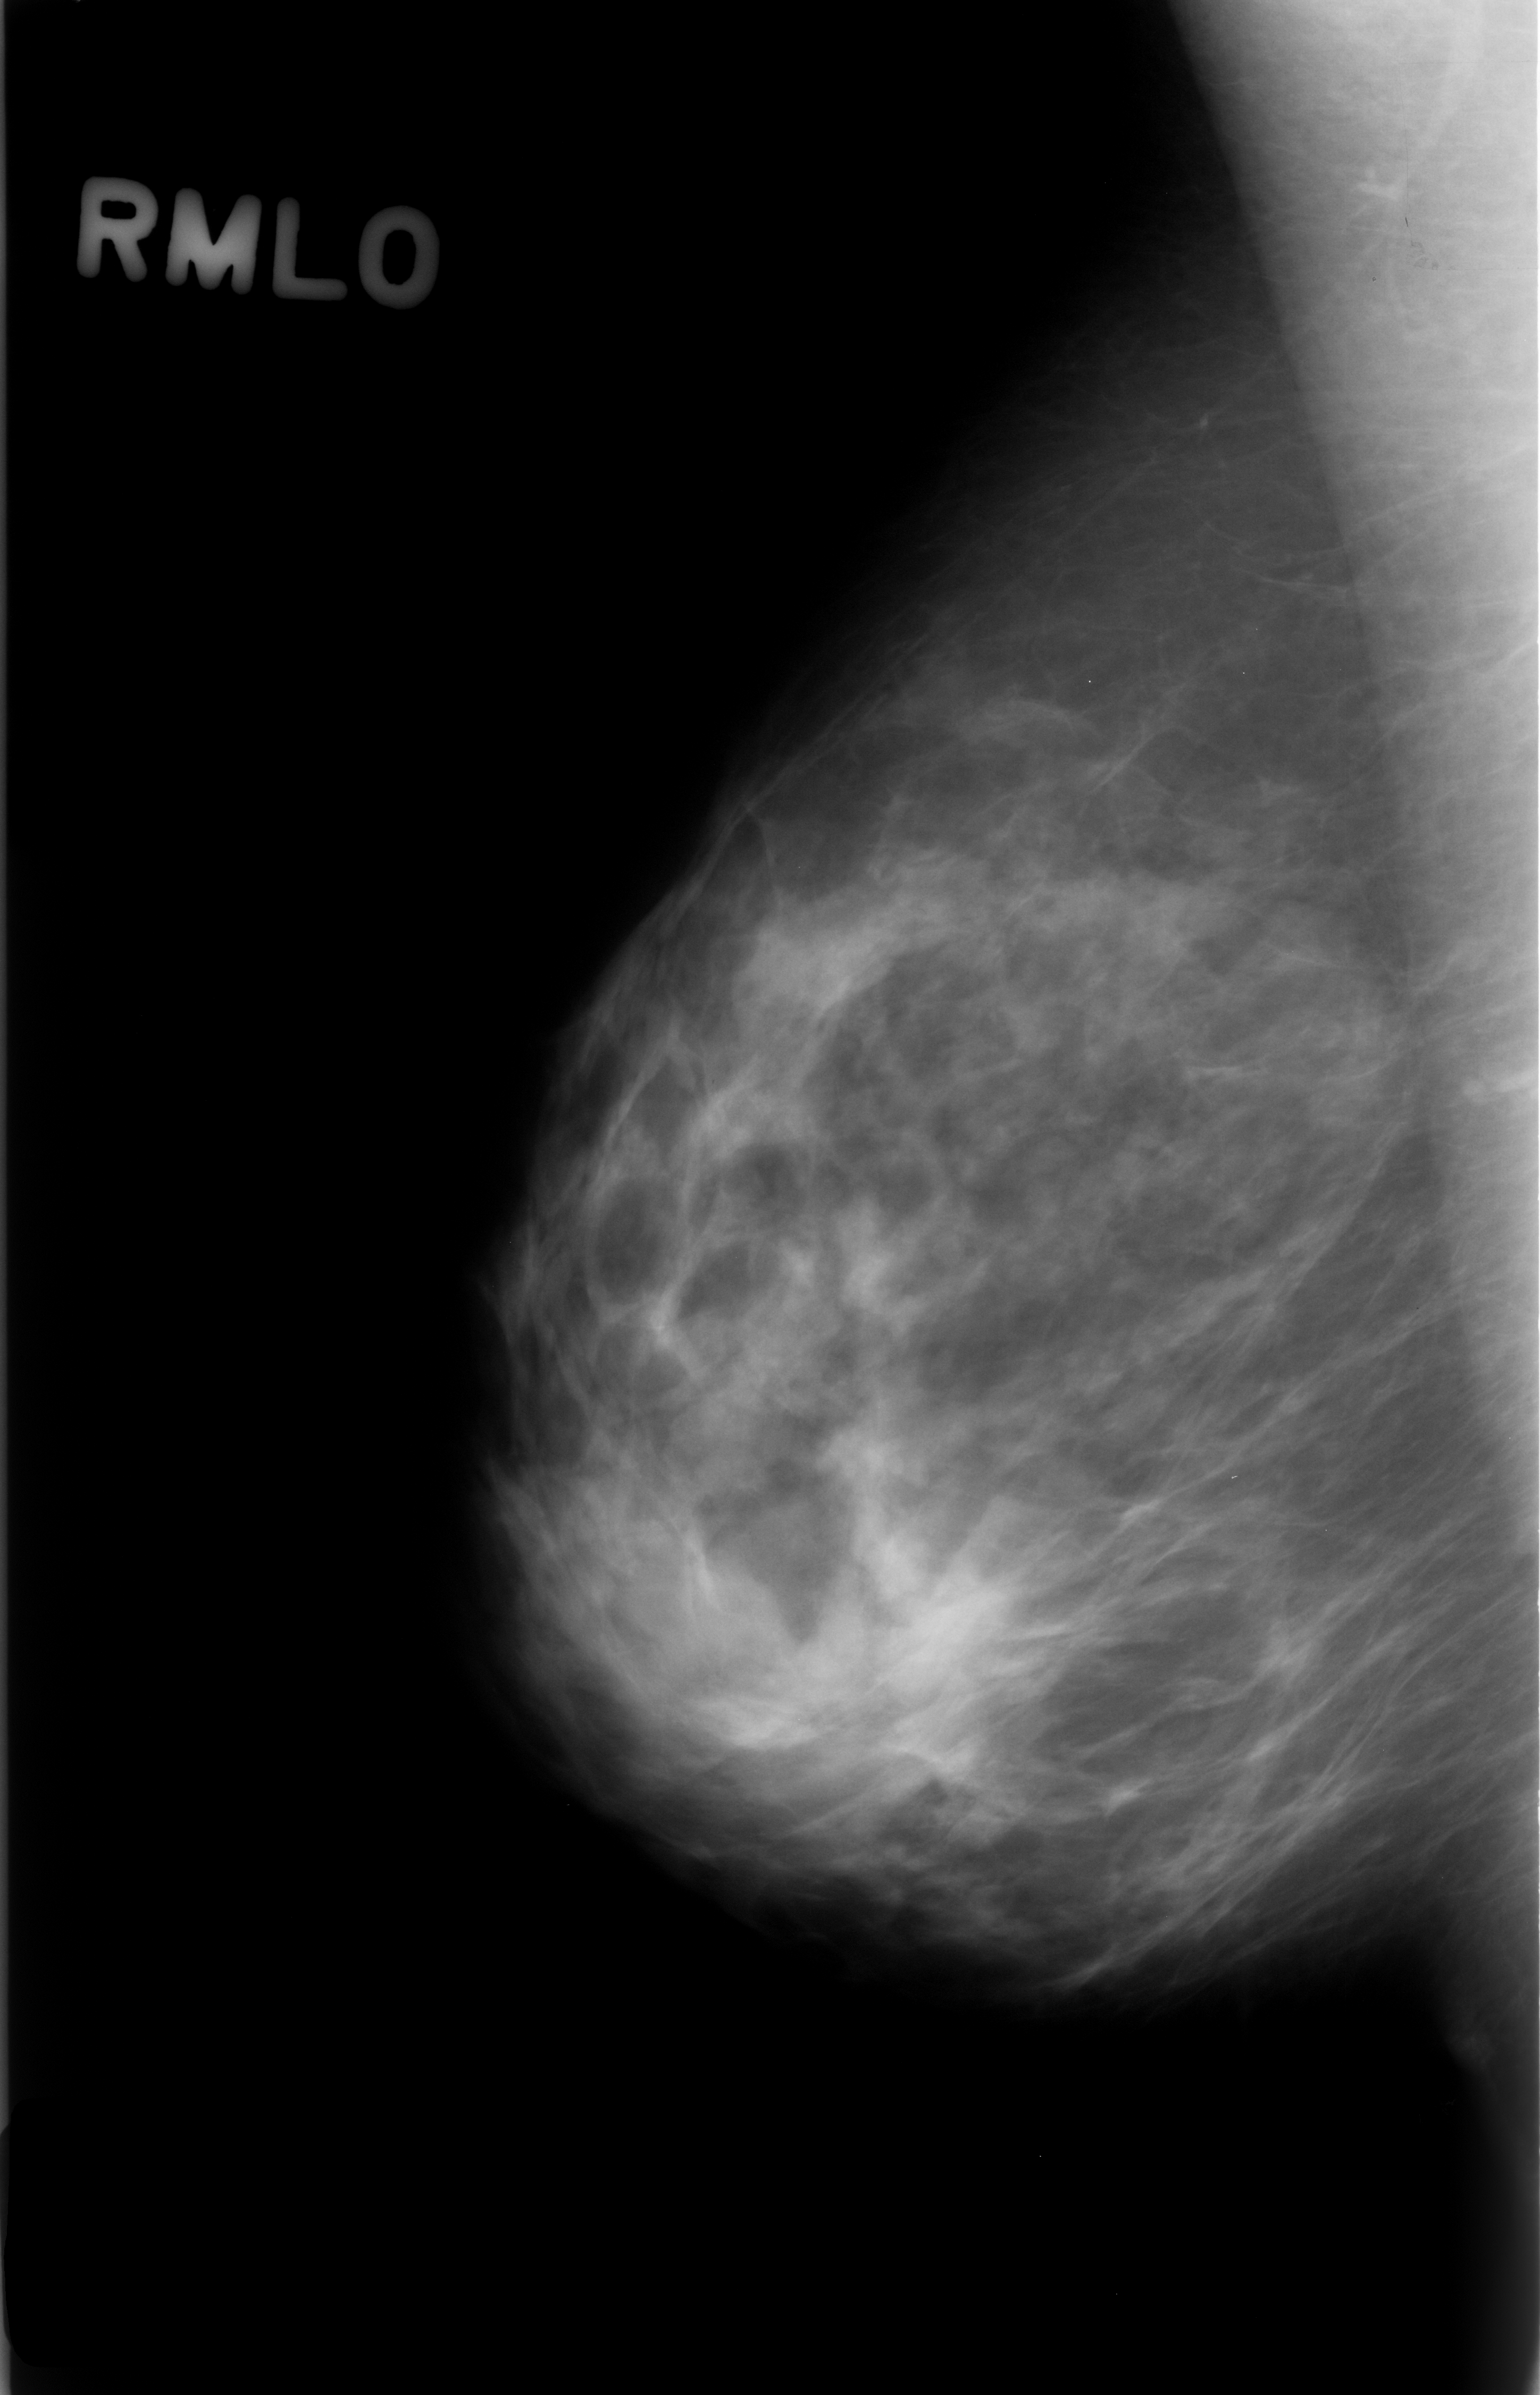
Mammogram (digitized film); right breast; MLO view; breast composition: scattered fibroglandular densities (BI-RADS density category 2 of 4); 1540 × 2395 image matrix.
Expert-marked regions of interest on this film, with their recorded descriptors:
- mass, shape focal asymmetric density; BI-RADS assessment category 3; subtlety rating 5 on a 1 (subtle) to 5 (obvious) scale; benign; no additional work-up was recommended (outcome (as recorded, no biopsy): benign without callback): bounding box (x1, y1, x2, y2) in pixels: (861, 1525, 1045, 1759)